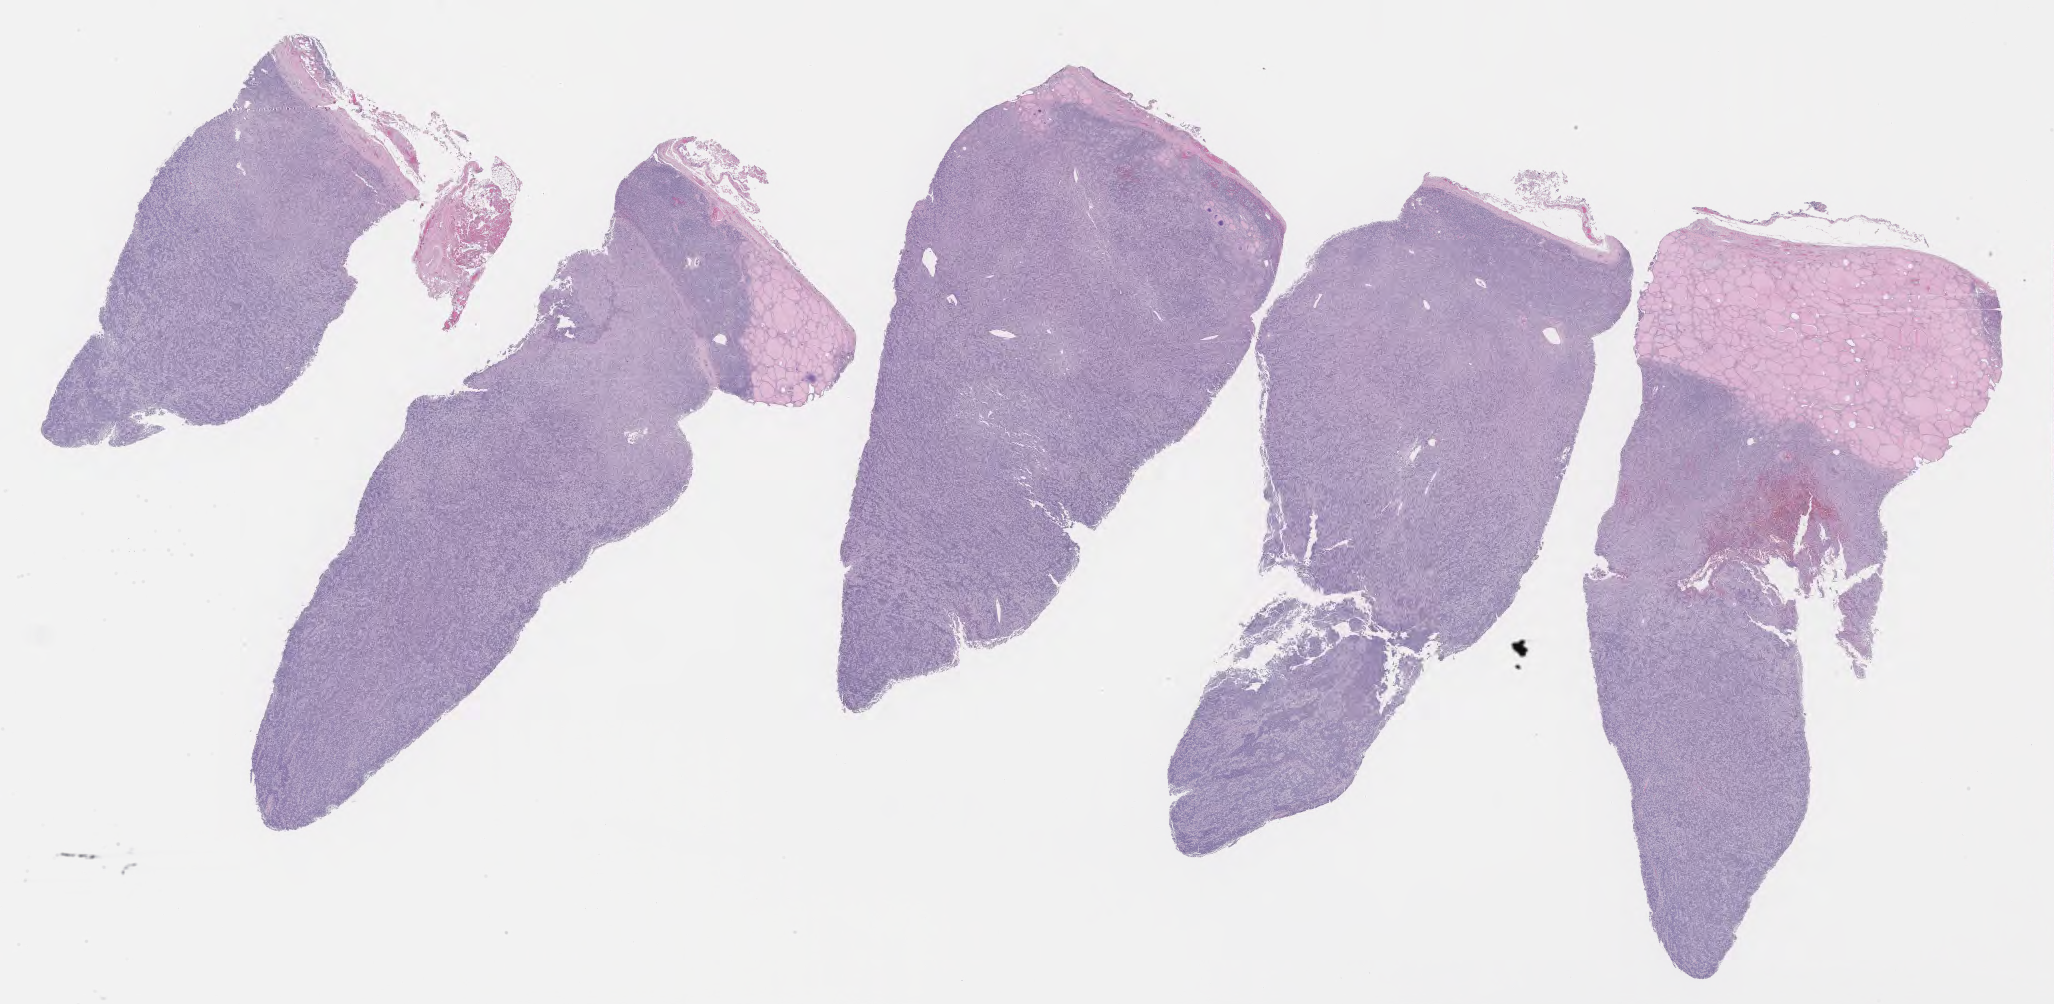
Whole-slide image, H&E stain — whole scanned area (about 33.2 x 16.2 mm) shown as a low-resolution overview; specimen: tumor tissue. Male patient, age 56 years.
Histologic diagnosis: Burkitt lymphoma, NOS.